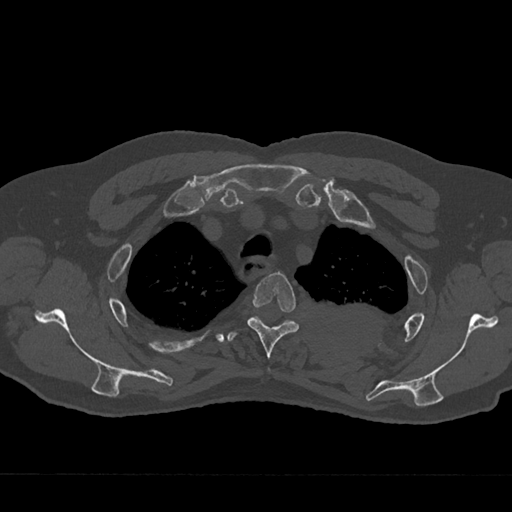
CT including the spine, one axial slice; bone window (W 1800 / L 400 HU); 0.5 mm slice thickness; 512 × 512 image matrix, field of view 377 × 377 mm. Male patient, age 75 years. Case-level facts recorded for this patient, not image findings: primary cancer: renal; vertebrae with lytic lesions (as recorded): T4.
Structures marked on this image (semi-automatic segmentation, software-assisted and operator-edited):
- T3 vertebra: bounding box [x1, y1, x2, y2] px = [247, 272, 299, 371]
- T4 vertebra: [227, 317, 290, 342]